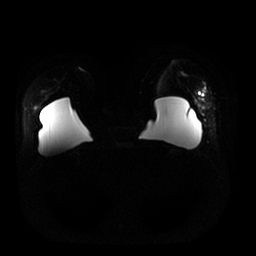
Breast MRI, one axial slice. Slice 8 of 25 in the series (ordered by position). Diffusion-weighted series; image 2 of 4 stored at this slice position (different b-values; order by instance number). 1.5 T. 256 × 256 image matrix, field of view 380 × 380 mm. Female patient.
Outlined on this slice (outlined manually by an expert reader):
- tumour on diffusion-weighted imaging: bounding box <205,93,213,105> (left, top, right, bottom; pixels)